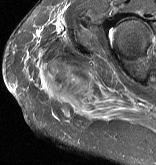
MRI of an extremity soft-tissue mass, one axial slice; position 42 of 57 along the scan axis; STIR; MR volume resampled by the dataset authors to the PET/CT grid (not the native acquisition matrix); 3.27 mm slice thickness; 156 × 165 image matrix, field of view 152 × 161 mm. Female patient. Case-level facts recorded for this patient, not image findings: histological type: epithelioid sarcoma with vascular differentiation; site of the primary tumour: right buttock.
Annotated regions visible in this slice (expert contour drawn on MRI and transferred to this co-registered scan by the dataset authors):
- gross tumour volume (mass): bounding box <38,59,91,99> (left, top, right, bottom; pixels)